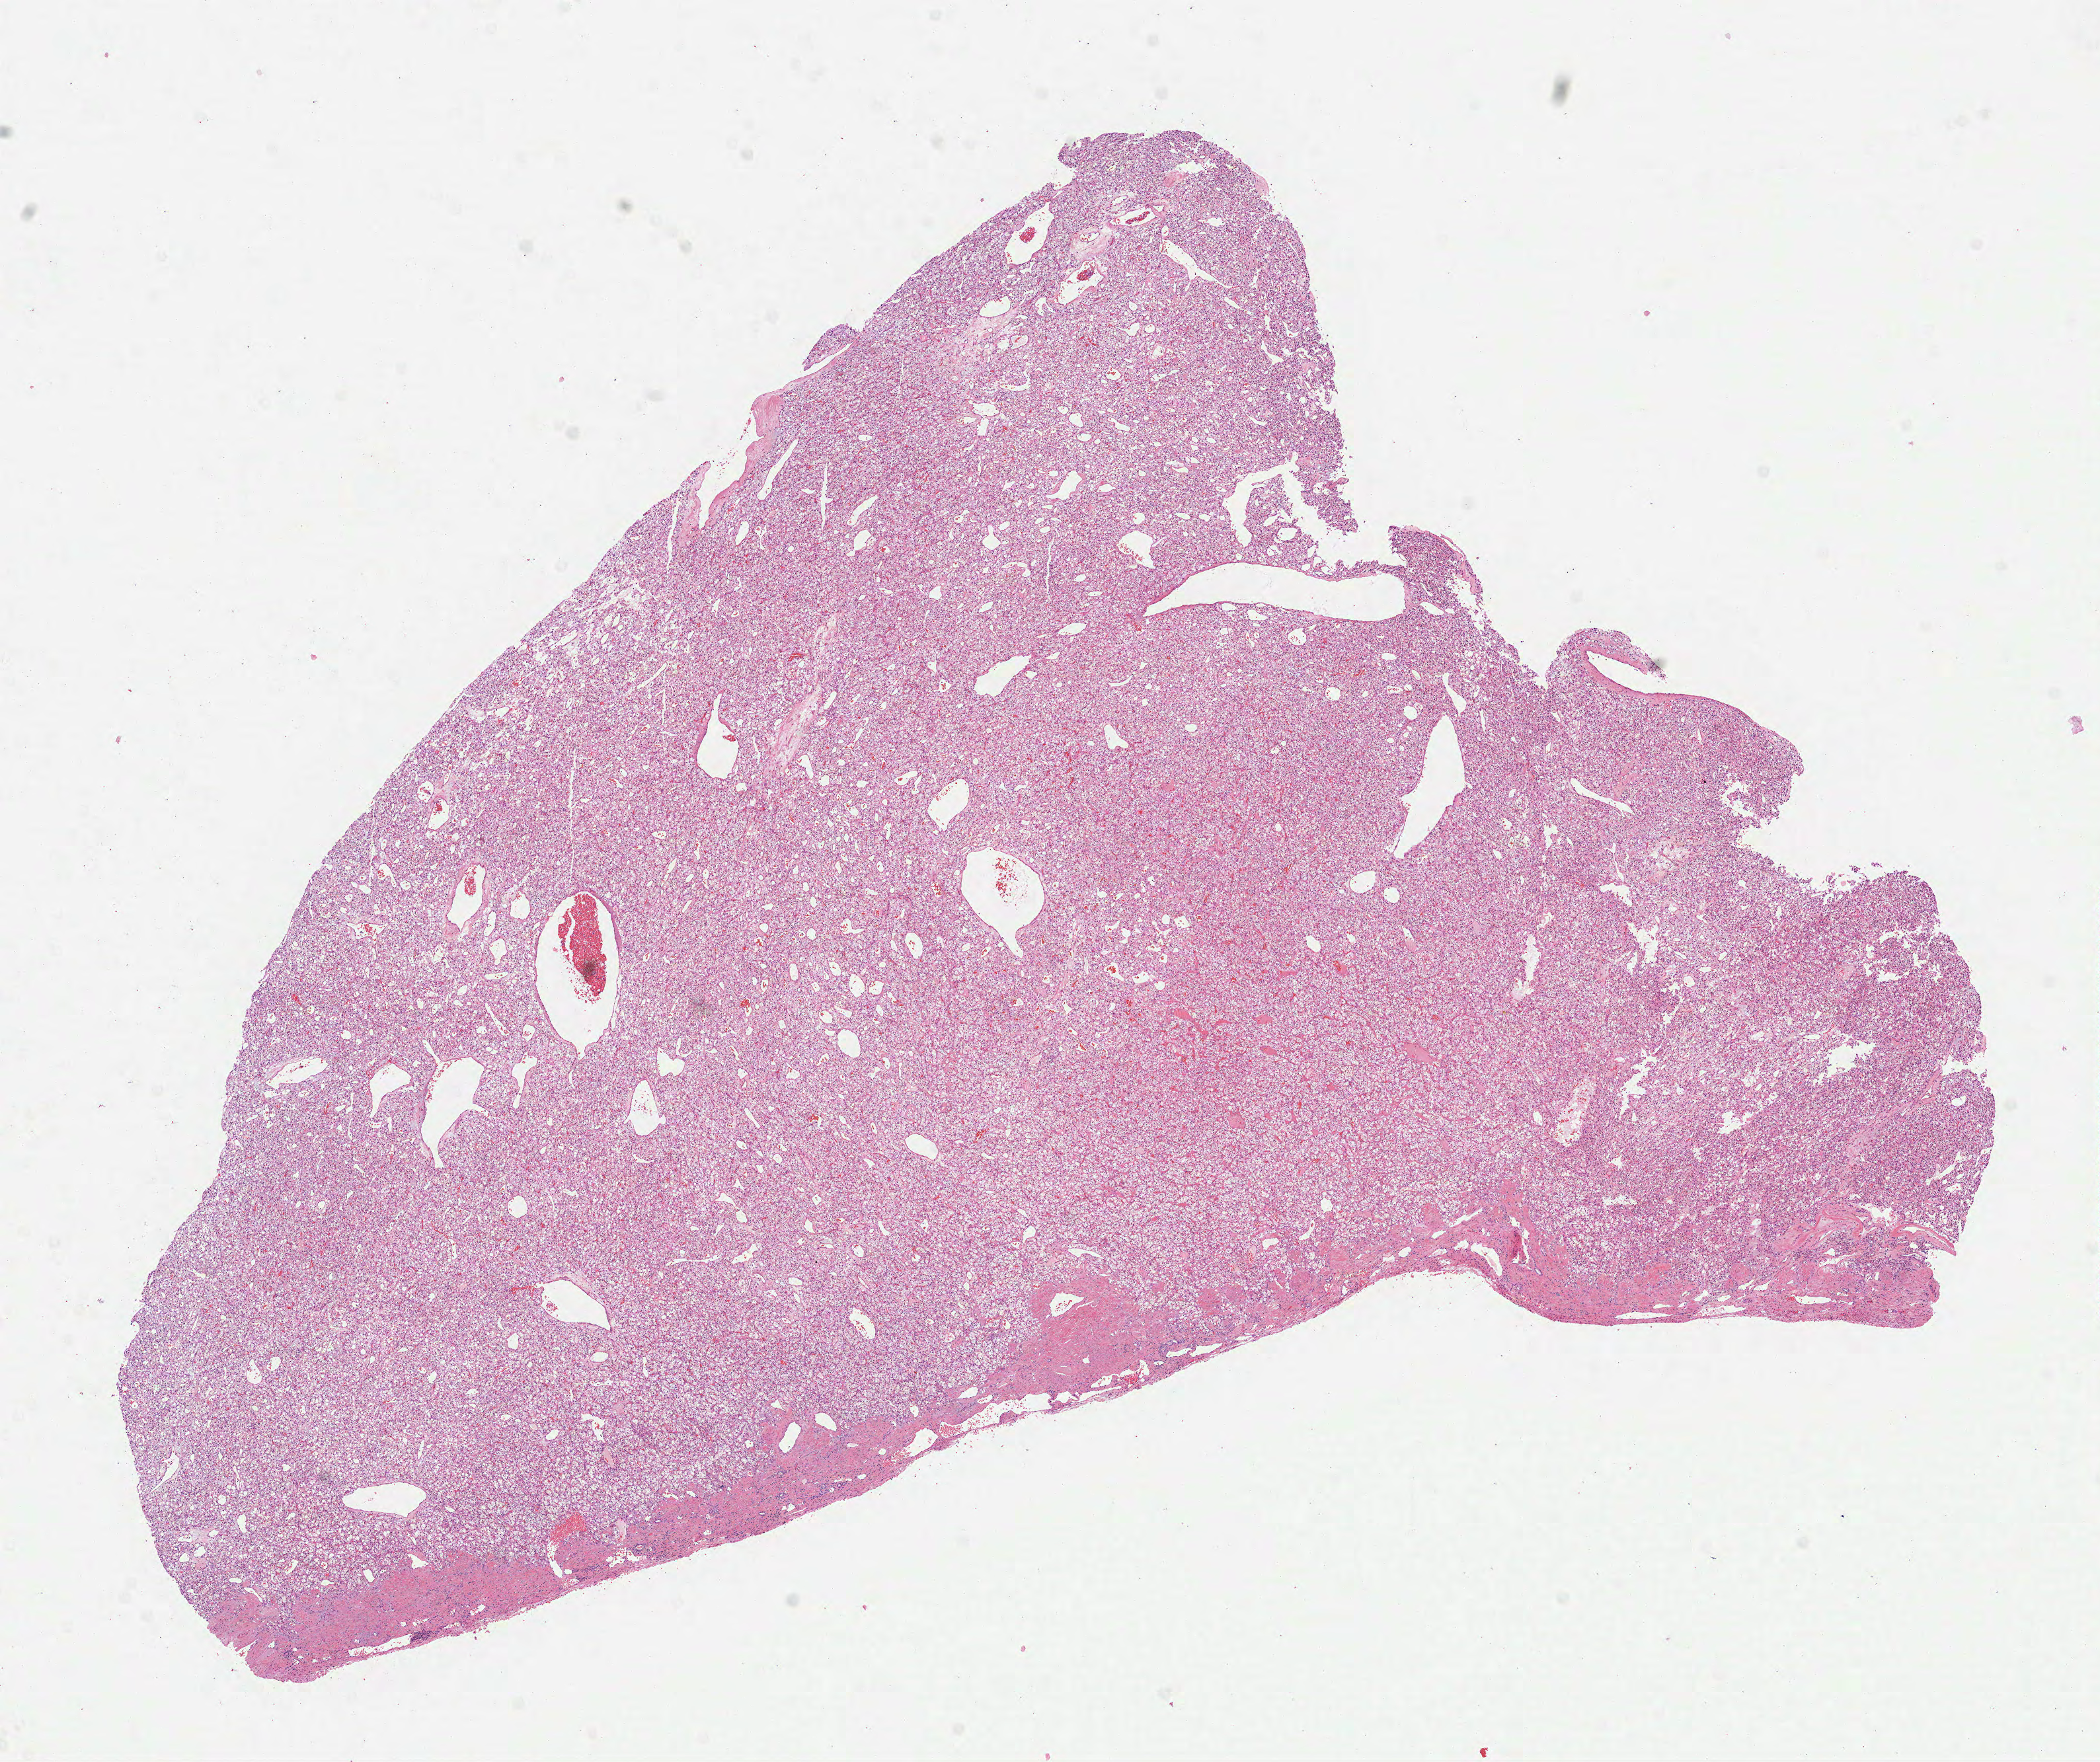
H&E whole-slide image — low-resolution overview of the scanned area, about 12.8 x 10.8 mm; formalin-fixed paraffin-embedded (FFPE) diagnostic section; kidney, primary tumour sample. Female patient. Histologic grade: G2 (moderately differentiated).
• AJCC pathologic stage: I
• pathologic diagnosis: Clear cell adenocarcinoma, NOS
• laterality: right